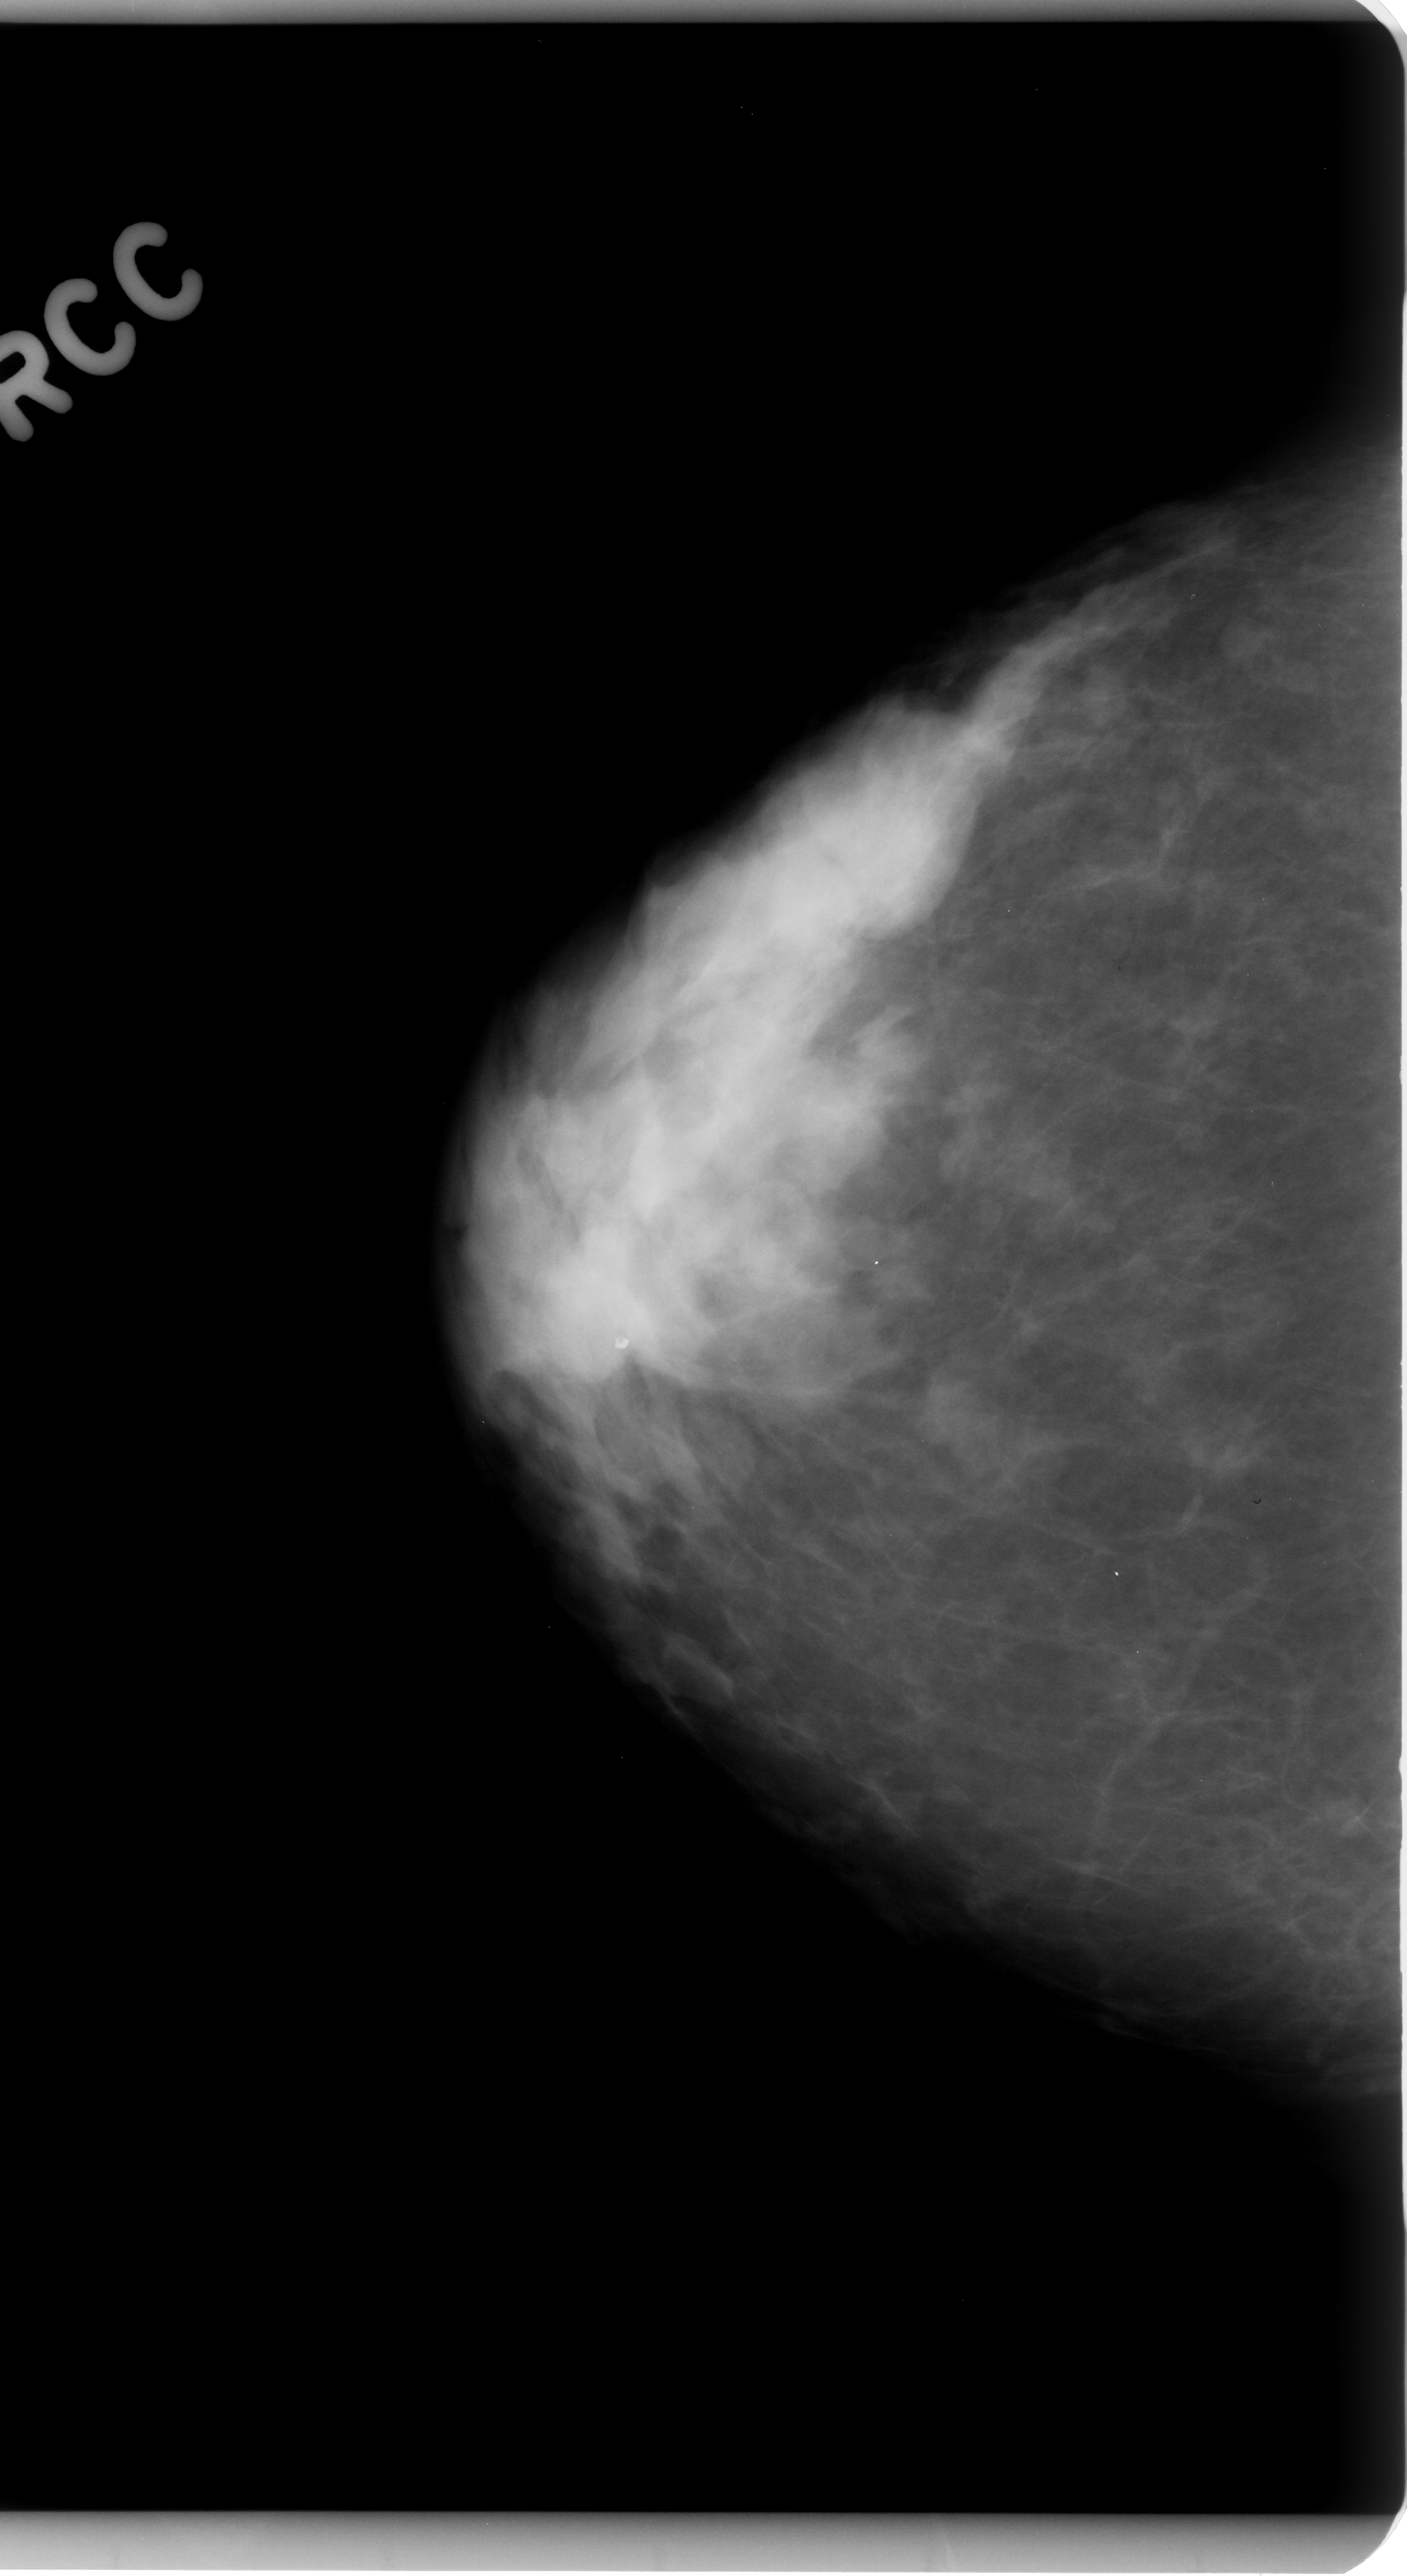
Scanned film-screen mammogram; right breast; craniocaudal (CC) view; breast composition: heterogeneously dense (BI-RADS density category 3 of 4); 1407 × 2576 image matrix.
Marked abnormalities (boxes around the expert regions of interest):
- mass, shape lobulated, margins ill defined; BI-RADS assessment category 3; pathology result (as recorded, not read from the image): benign: bounding box [x1, y1, x2, y2] px = [754, 735, 972, 965]